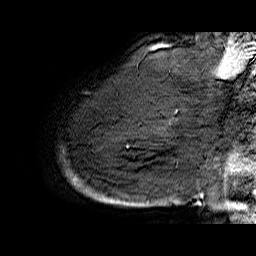
Breast MRI (dynamic contrast-enhanced), one sagittal slice. Position 52 of 60 along the scan axis. Dynamic contrast-enhanced series, time point 2 of 6 at this slice position (early post-contrast). 1.5 T. TE 6.4 ms, TR 32.9 ms. 4 mm slice thickness. 256 × 256 image matrix. Female patient. Case-level facts recorded for this patient, not image findings: setting: breast cancer imaged before/during neoadjuvant chemotherapy; receptor status: HR-positive, HER2-negative.
Annotated regions visible in this slice (semi-automatic segmentation, software-assisted and operator-edited):
- analysis volume of interest (the breast-tissue region the enhancement analysis was run in; not a lesion): bounding box [x1, y1, x2, y2] px = [61, 74, 176, 208]
- tumour enhancement mask (voxels above the 100 % enhancement threshold inside the analysis volume of interest): [72, 111, 176, 181]